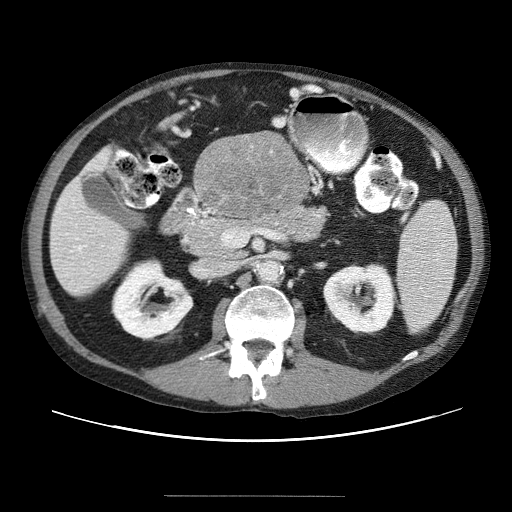
Contrast-enhanced abdominal CT (liver protocol), one axial slice; position 10 of 69 along the scan axis; soft-tissue window (W 400 / L 40 HU); 2.5 mm slice thickness; 512 × 512 image matrix, field of view 380 × 380 mm. From the clinical record (not read from this slice): diagnosis: hepatocellular carcinoma (patient treated with transarterial chemoembolisation; whether this scan precedes or follows treatment is not stated here); TNM stage (as recorded): Stage-IVB; Child-Pugh class: B; tumour differentiation: poorly differentiated.
Outlined on this slice (semi-automatically segmented with operator editing):
- liver parenchyma outside the tumour (the mass and vessels are separate outlines, so this box may not span the whole liver): bounding box [x1, y1, x2, y2] px = [50, 136, 306, 292]
- mass: [194, 135, 310, 223]
- liver vessels: [62, 216, 103, 283]